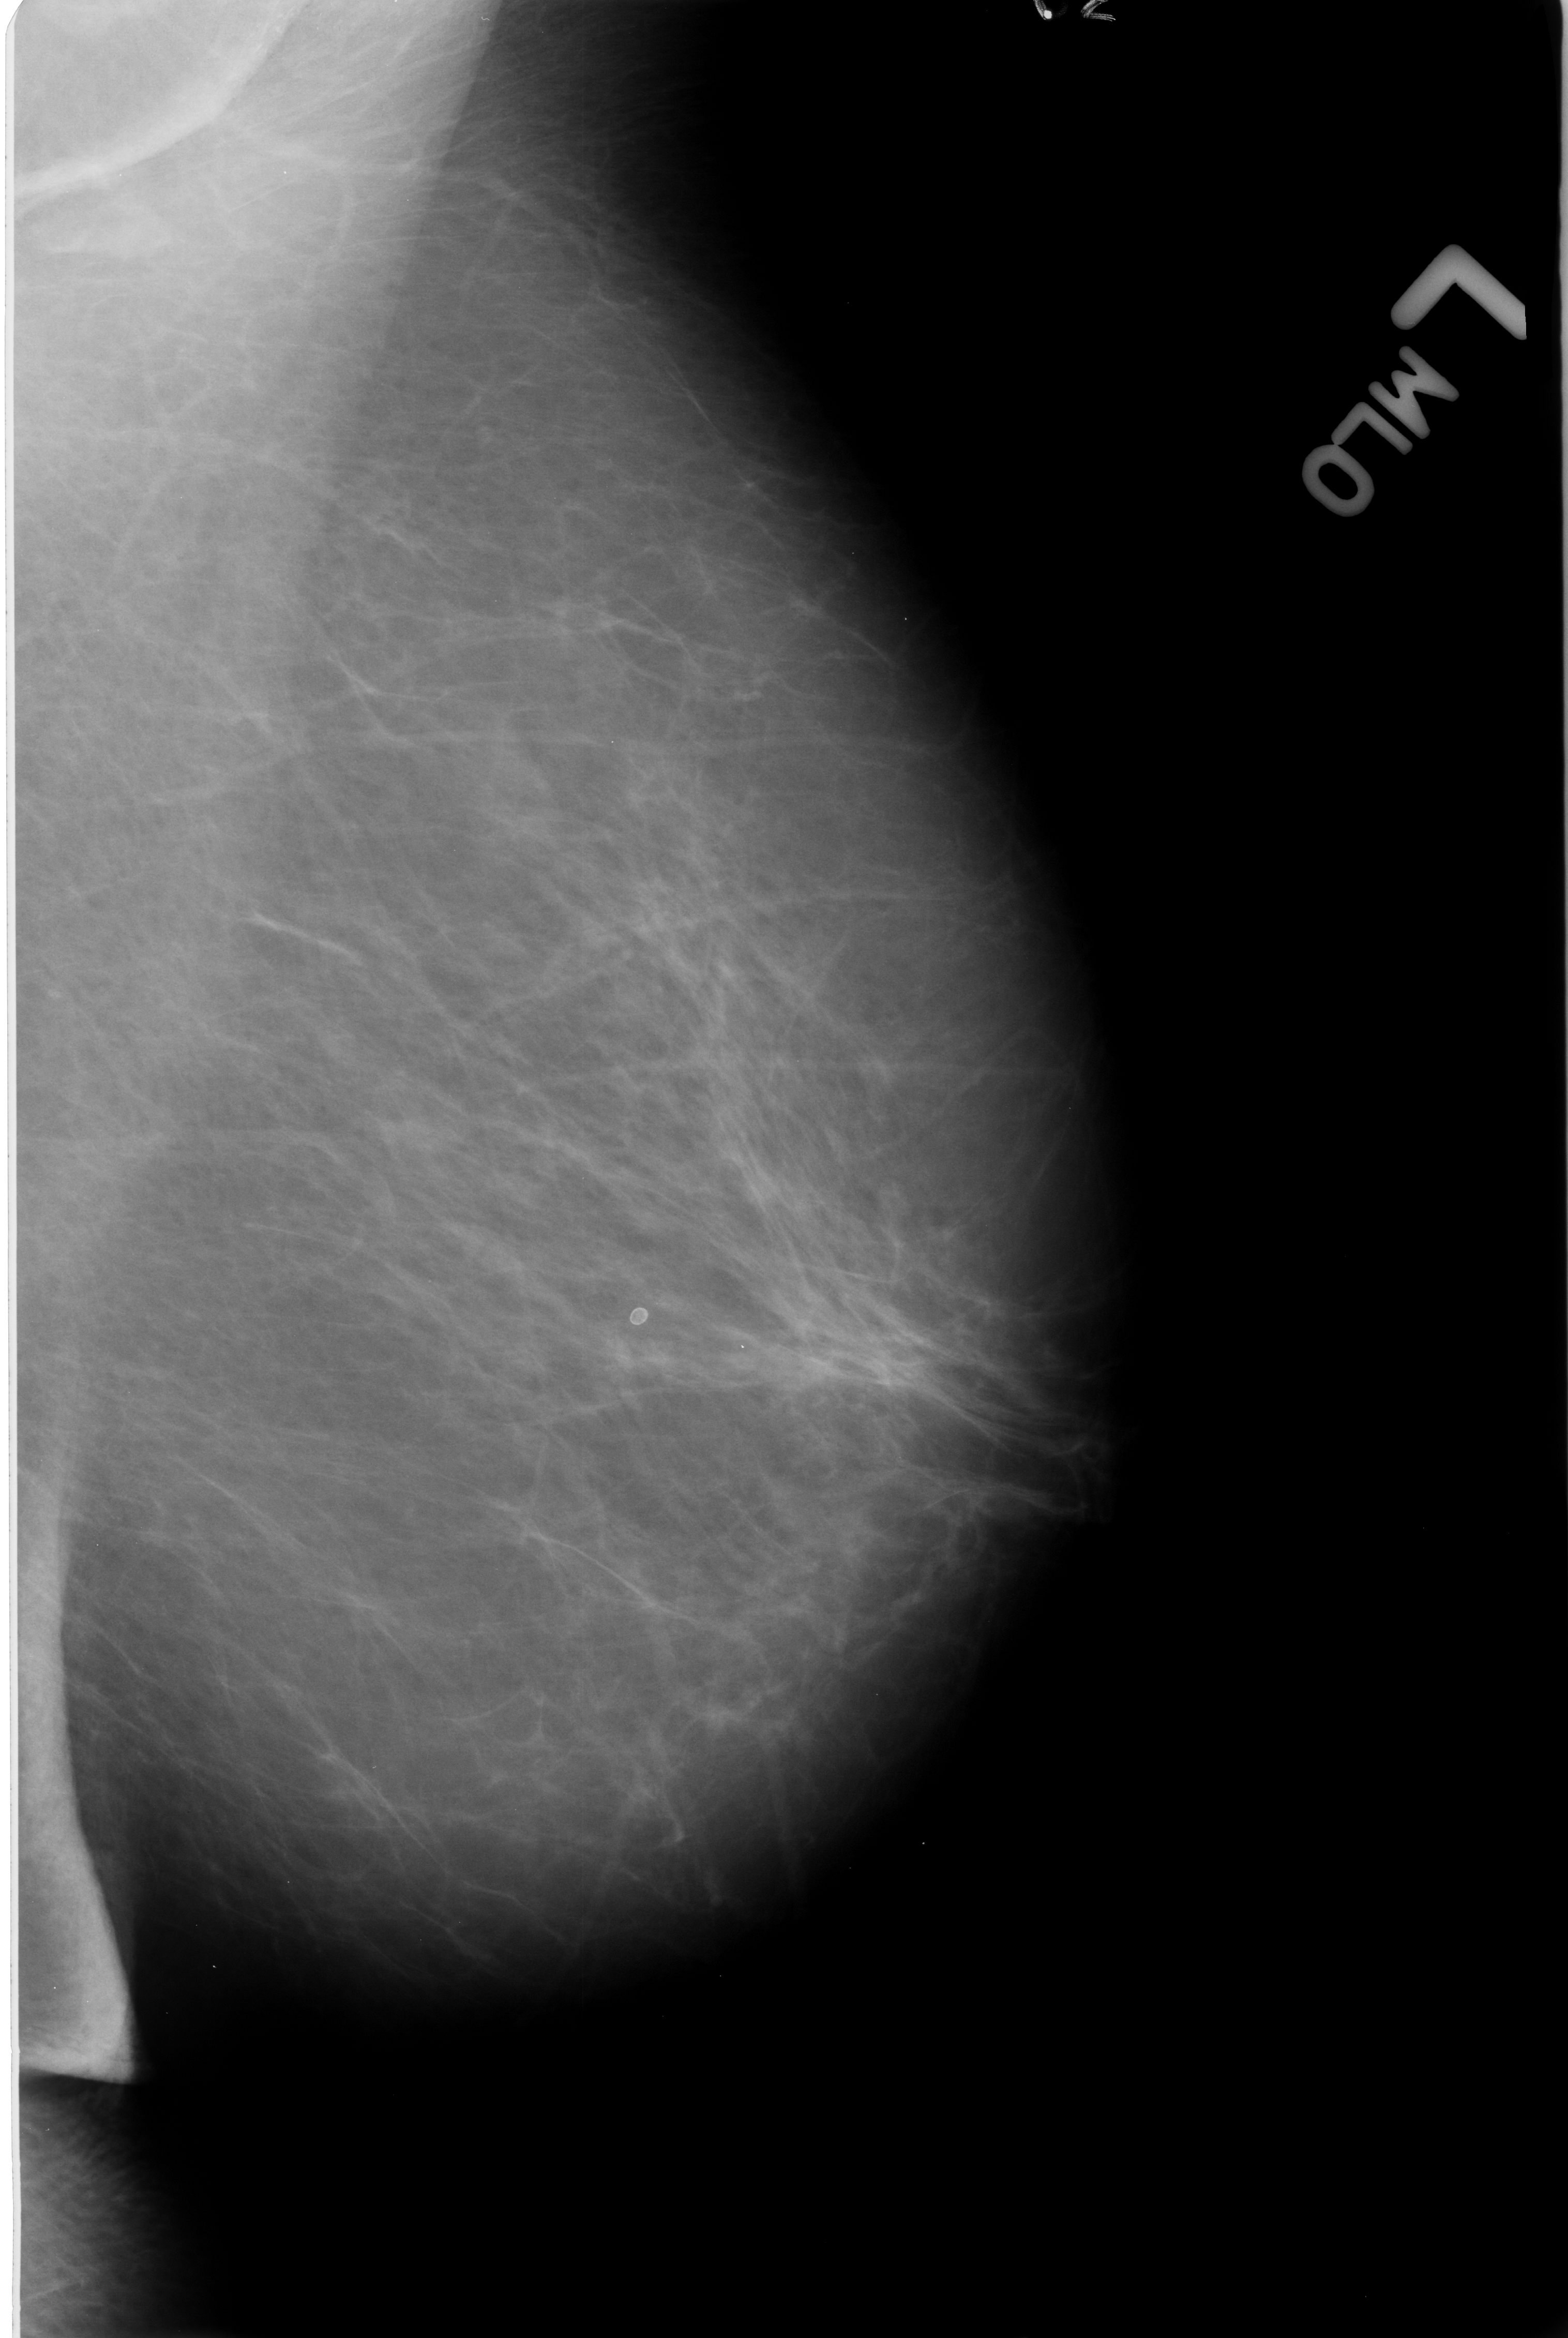
Mammogram (digitized film); left breast; mediolateral oblique (MLO) view; BI-RADS breast density category 2 (scale 1–4).
Abnormality record for this image: calcifications, morphology lucent center; BI-RADS assessment category 2; subtlety rating 4 on a 1 (subtle) to 5 (obvious) scale; benign without callback (not worked up further).